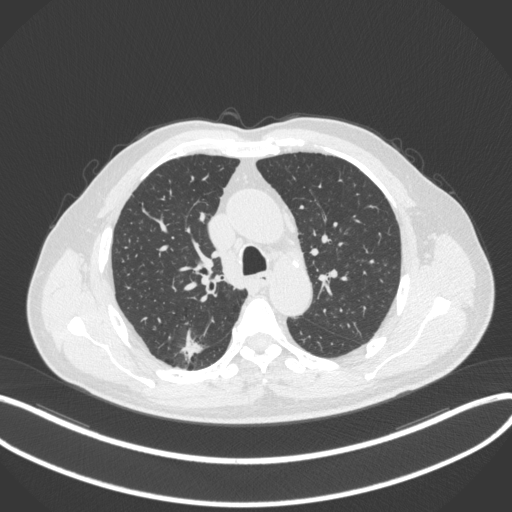
Chest CT, one axial slice; slice 258 of 366 in the series (ordered by position); reconstruction kernel B31f; 120 kVp; lung window (W 1500 / L -600 HU); 512 × 512 image matrix, field of view 400 × 400 mm. Male patient, age 69 years. From the clinical record (not read from this slice): clinical TNM (as recorded): T1b N0 M0; histopathological grade: G2-3.
Outlined on this slice (bounding box drawn by a radiologist):
- lung tumour (recorded histology: adenocarcinoma): box from (x=176, y=331) to (x=202, y=362) px